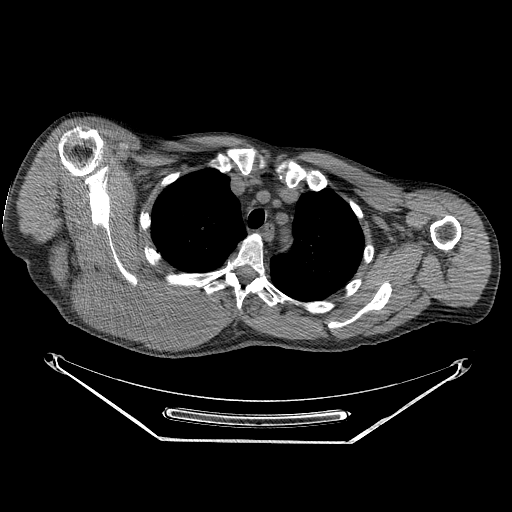
CT of an extremity soft-tissue mass (from a PET/CT study), one axial slice. Slice 192 of 267 in the series (ordered by position). Reconstruction kernel STANDARD. 140 kVp. Soft-tissue window (W 400 / L 40 HU). 512 × 512 image matrix. Male patient. From the clinical record (not read from this slice): histological type: pleiomorphic spindle cell undifferentiated; grade: high; site of the primary tumour: right parascapusular.
Structures marked on this image (expert contour drawn on MRI and transferred to this co-registered scan by the dataset authors):
- gross tumour volume including surrounding oedema: bounding box (x1, y1, x2, y2) in pixels: (78, 260, 229, 339)
- gross tumour volume (mass): (78, 260, 211, 336)